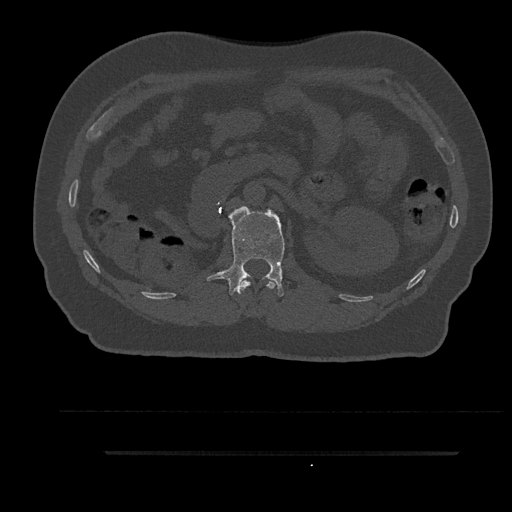
CT including the spine, one axial slice. Slice 185 of 797 in the series (ordered by position). Reconstruction kernel Br40s/3. 120 kVp. Bone window (W 1800 / L 400 HU). 512 × 512 image matrix, field of view 432 × 432 mm. Male patient, age 63 years. From the clinical record (not read from this slice): primary cancer: renal.
Structures marked on this image (semi-automatic segmentation, software-assisted and operator-edited):
- L1 vertebra: bounding box (x1, y1, x2, y2) in pixels: (207, 207, 285, 296)
- T12 vertebra: (240, 280, 277, 292)